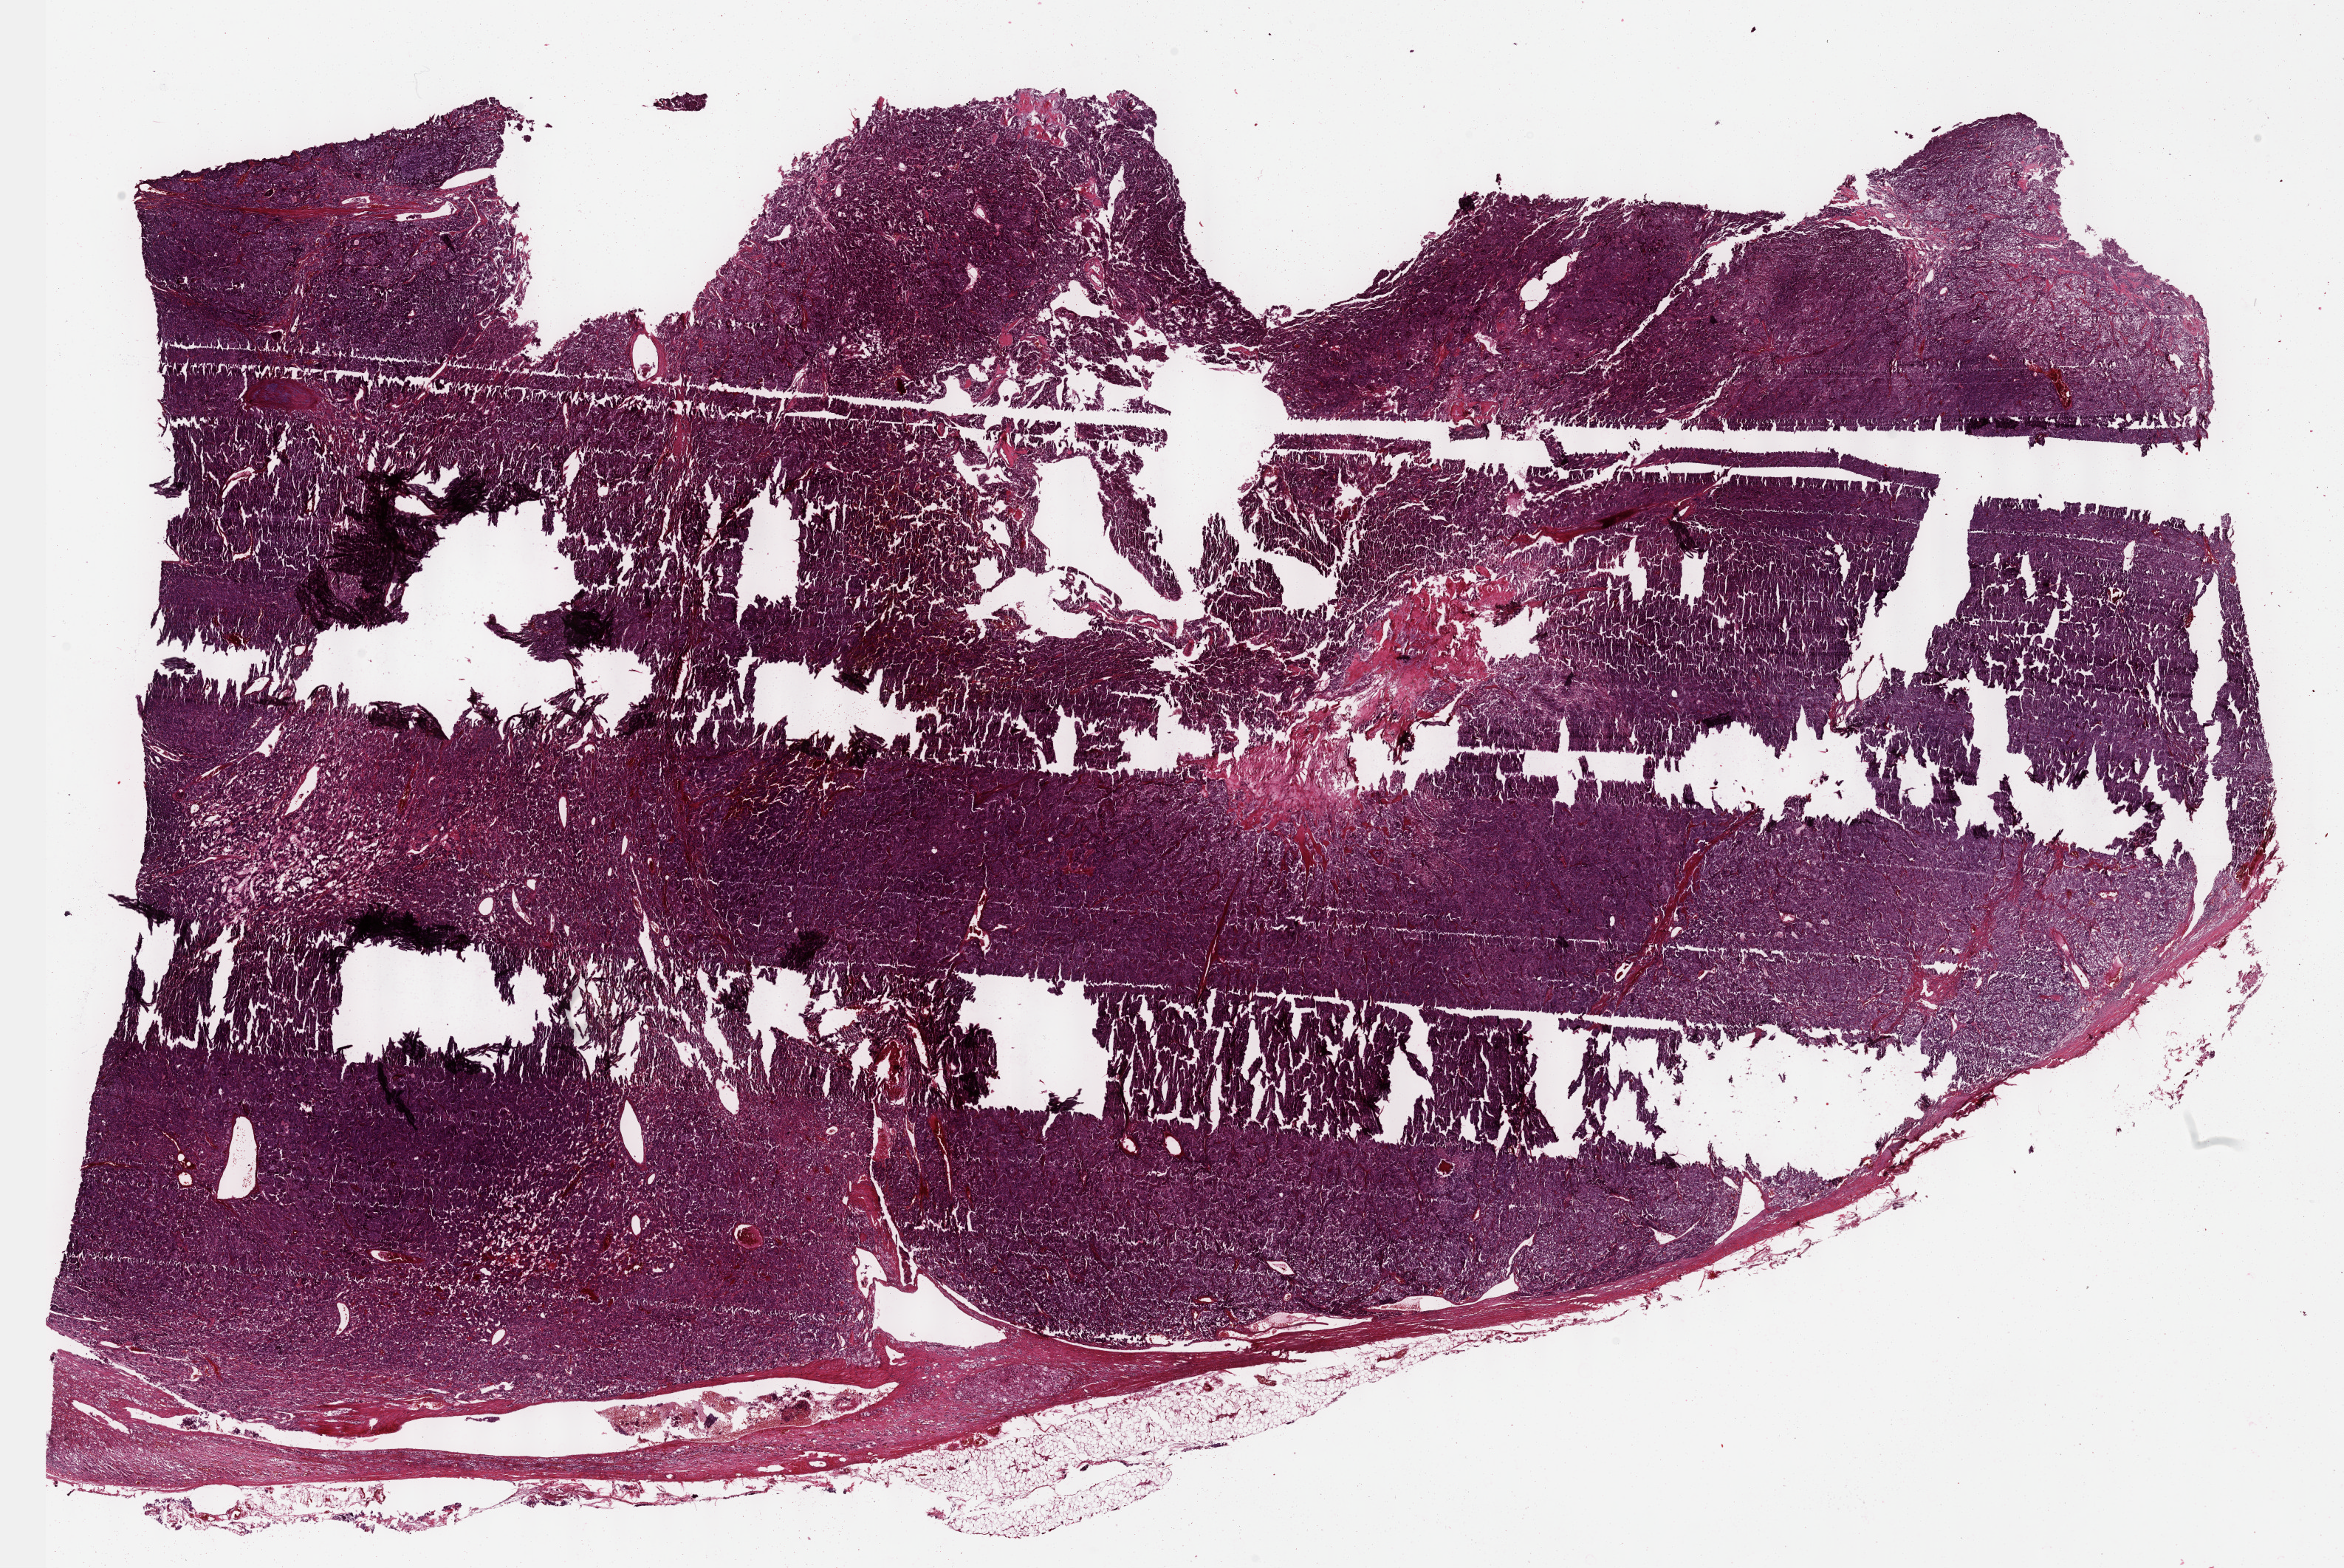
Digitized H&E-stained tissue section (whole slide) — whole scanned area (about 25.7 x 17.2 mm, from a 40x scan) shown as a low-resolution overview. FFPE section. Primary tumour sample from the adrenal gland. Male patient; age at initial diagnosis 37 years.
Diagnosis: Pheochromocytoma, NOS.